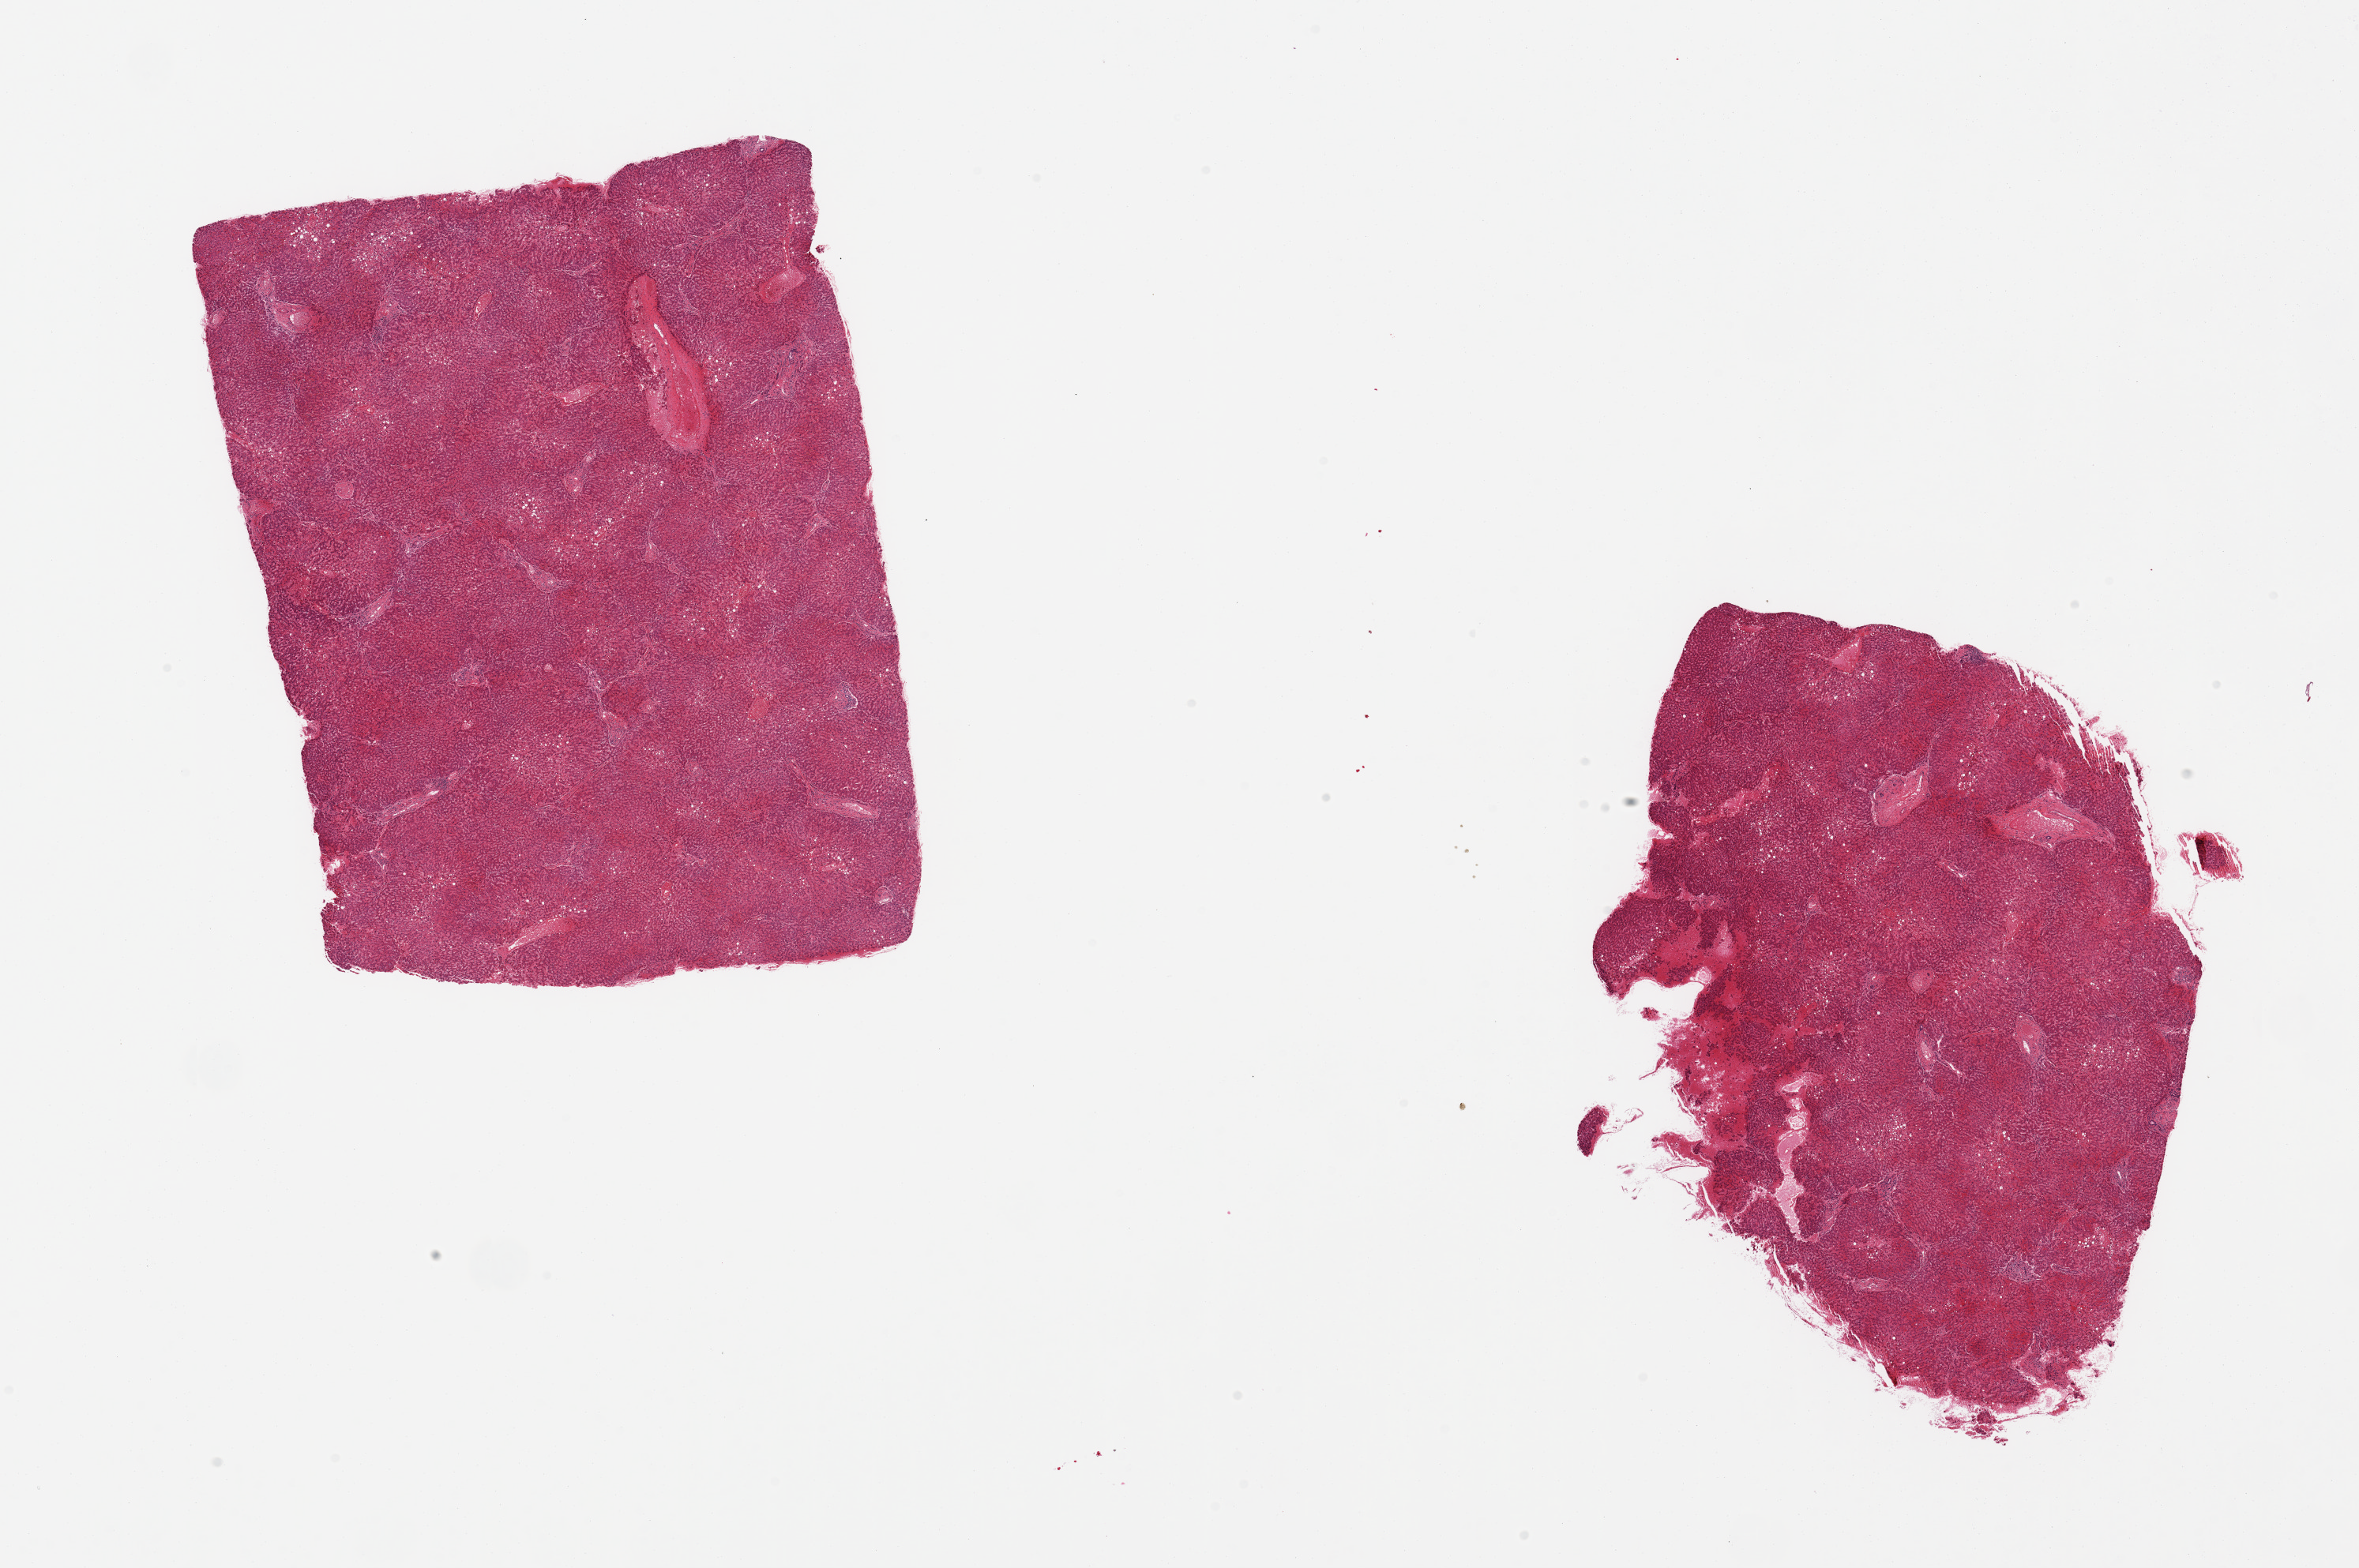
Whole-slide image, H&E stain — shown as a low-resolution overview of the whole scanned area (about 23.6 x 15.7 mm). PAXgene-fixed paraffin-embedded (PFPE) section. Sampled site (target tissue): liver. Donor tissue sample. Male donor.
Reviewer comment on this tissue sample: 2 pieces, mild congestion; ~10% macrovesicular parenchymal fat.